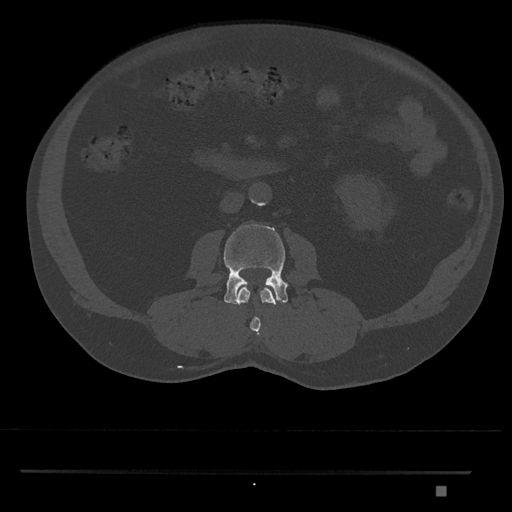
CT including the spine, one axial slice. Slice 706 of 1134 in the series (ordered by position). Reconstruction kernel Br40s/3. Bone window (W 1800 / L 400 HU). 0.5 mm slice thickness. 512 × 512 image matrix. Male patient, age 65 years. Case-level facts recorded for this patient, not image findings: primary cancer: prostate.
Outlined on this slice (semi-automatic segmentation, software-assisted and operator-edited):
- L2 vertebra: bounding box <238,287,276,335> (left, top, right, bottom; pixels)
- L3 vertebra: <223,224,288,305>